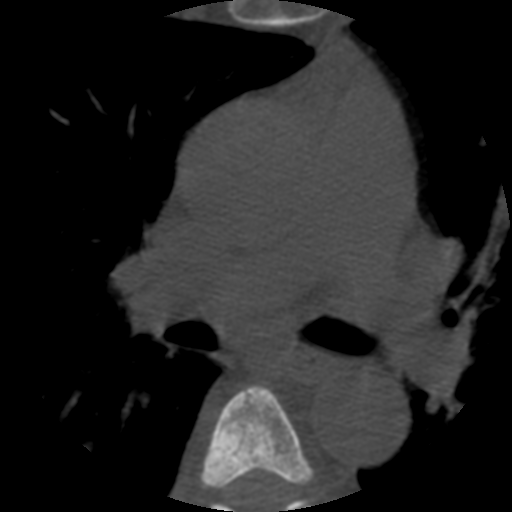
CT including the spine, one axial slice; slice 371 of 508 in the series (ordered by position); bone window (W 1800 / L 400 HU); 512 × 512 image matrix, field of view 160 × 160 mm. Patient age 57 years. Case-level facts recorded for this patient, not image findings: primary cancer: prostate.
Annotated regions visible in this slice (semi-automatic segmentation, software-assisted and operator-edited):
- T5 vertebra: bounding box (x1, y1, x2, y2) in pixels: (200, 386, 314, 490)
- T6 vertebra: (210, 498, 310, 512)